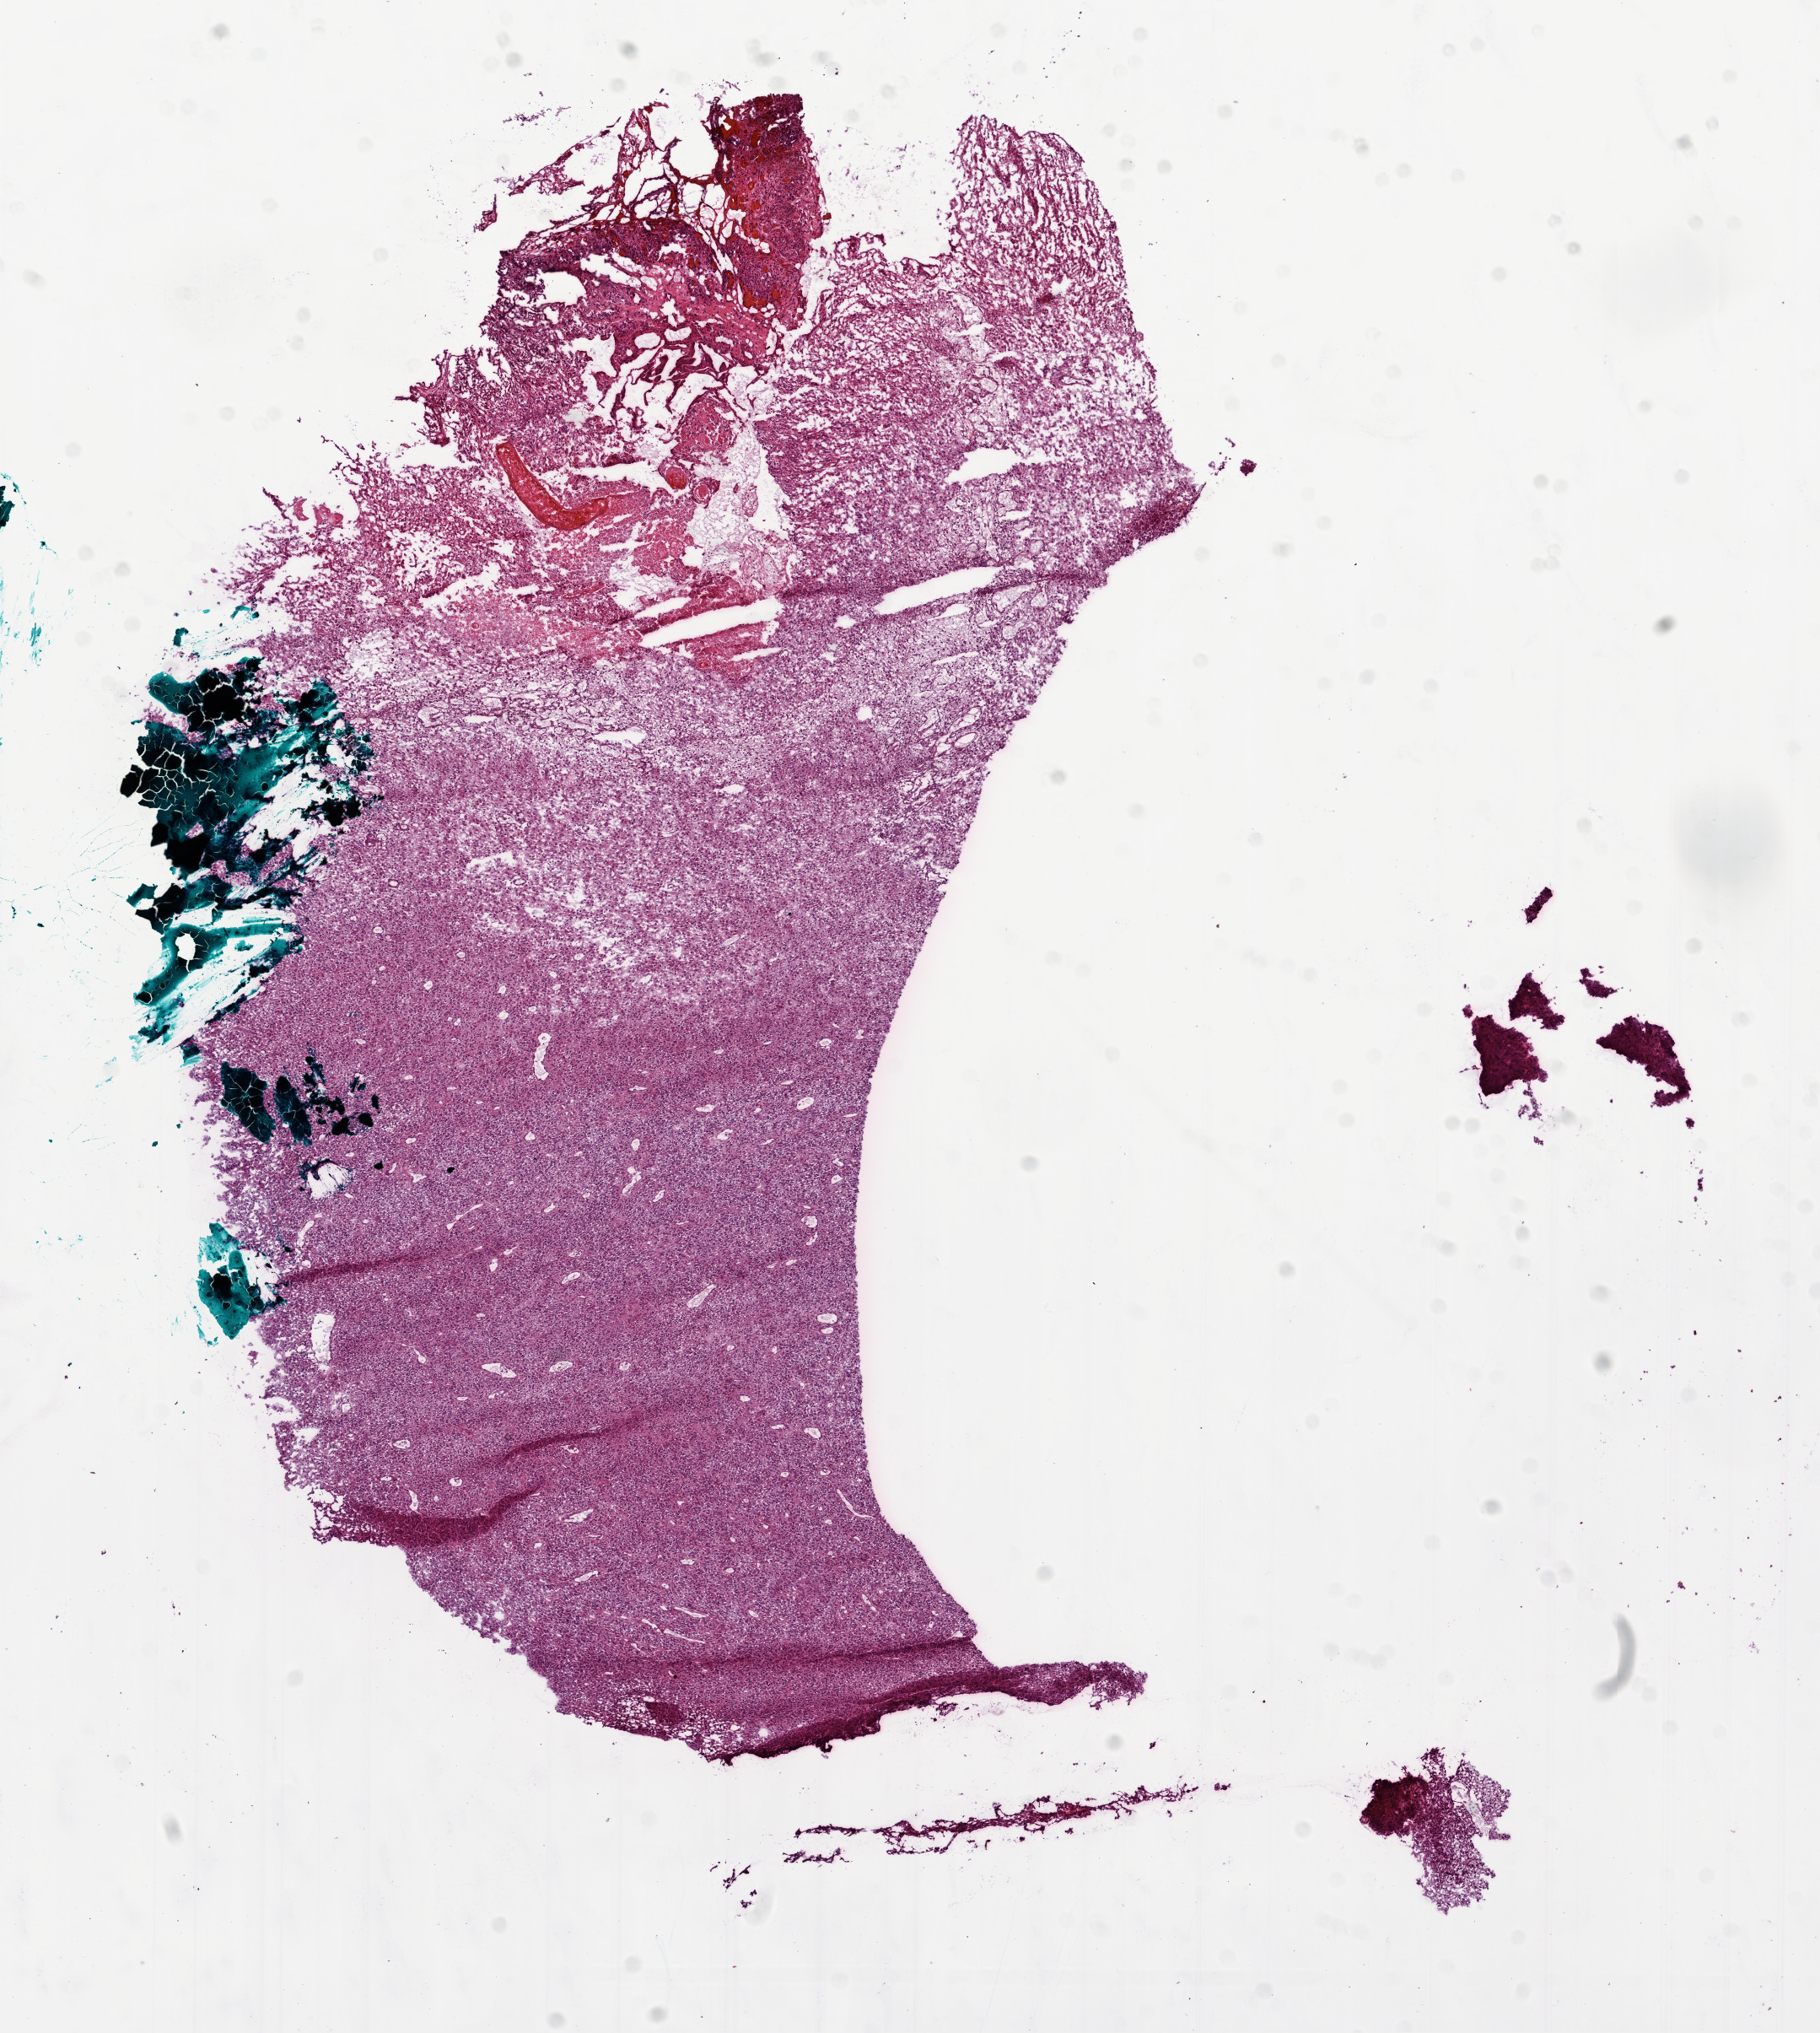
Digitized H&E-stained tissue section (whole slide) — low-resolution overview of the scanned area, about 8.7 x 9.7 mm (from a 20x scan); frozen section; primary tumour sample from the brain. Female, age 56 years at initial diagnosis. Composition of this section per pathologist review: tumour cells 80%, tumour nuclei 95%, normal cells 0%, stromal cells 10%, necrosis 10%.
Histologic diagnosis: Glioblastoma.